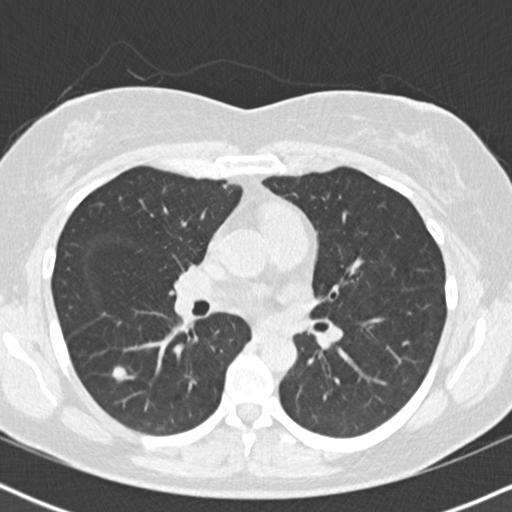
Low-dose screening chest CT, one axial slice. Slice 94 of 167 in the series (ordered by position). Reconstruction kernel B30f. Lung window (W 1500 / L -600 HU). 2 mm slice thickness. 512 × 512 image matrix, field of view 320 × 320 mm.
Structures marked on this image (manually delineated by an expert):
- lesion 1 (tumor, lower lobe of right lung): bounding box <112,366,128,382> (left, top, right, bottom; pixels)